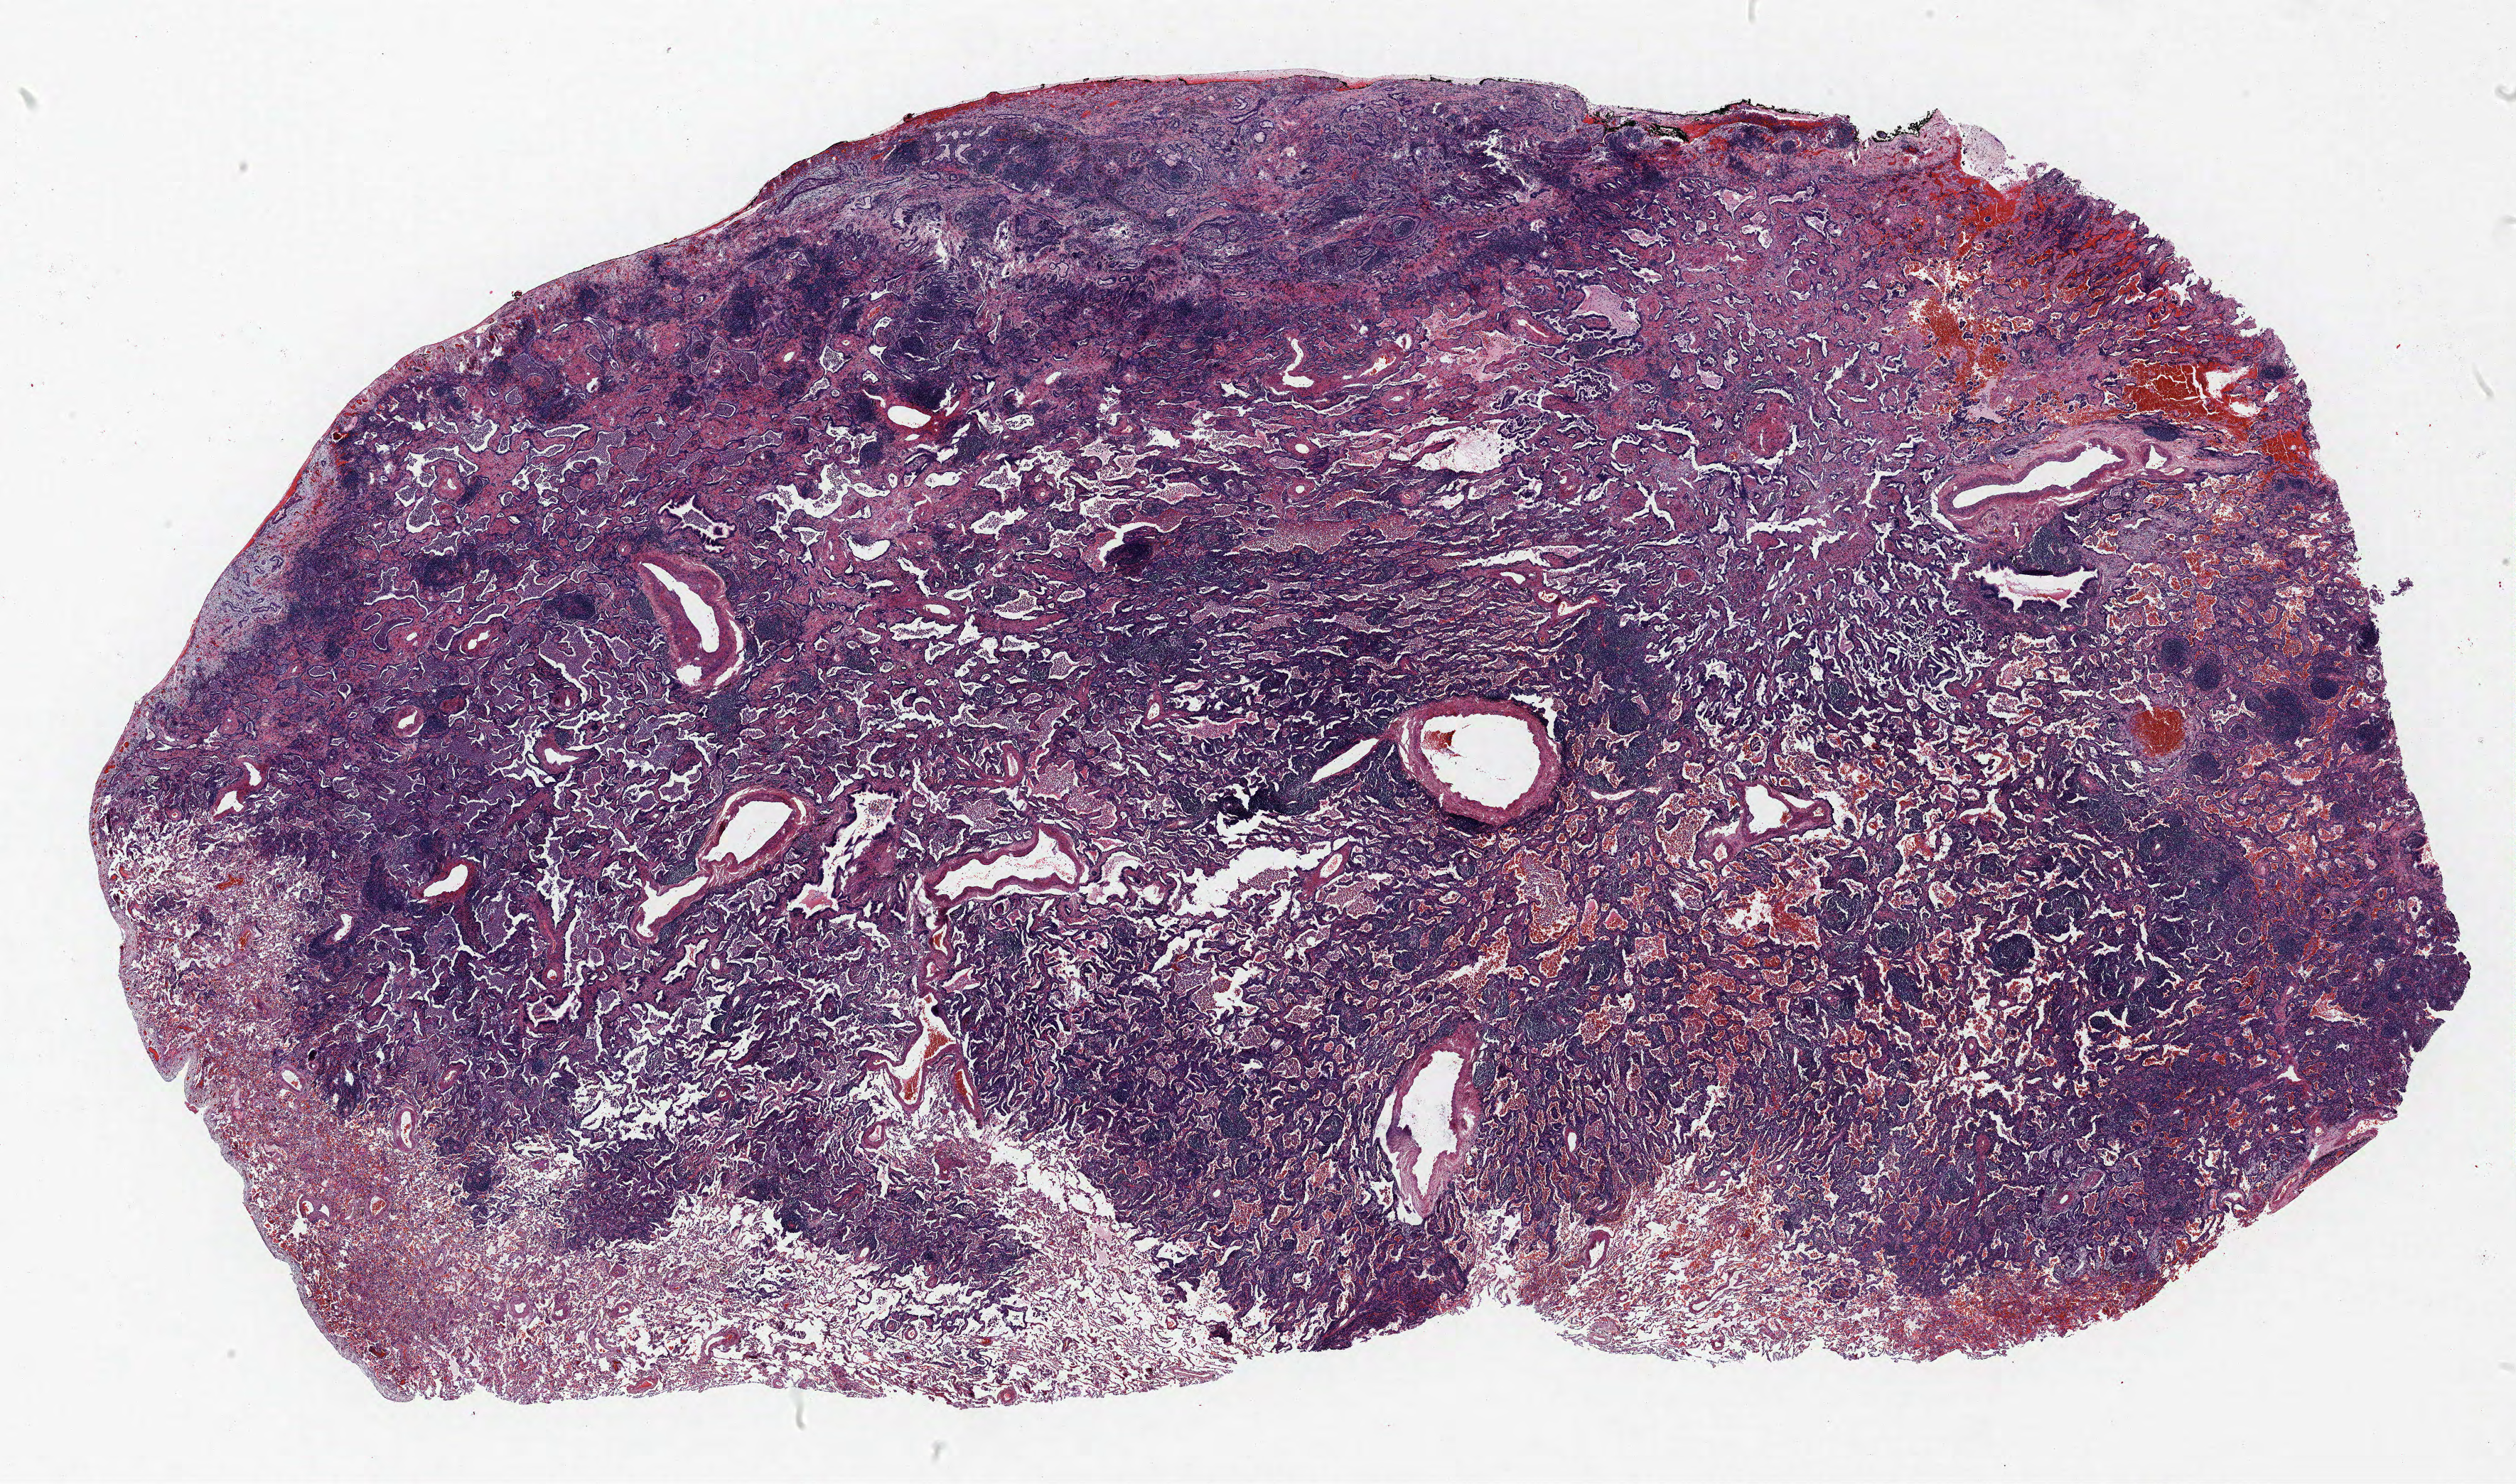
Whole-slide histology image, Hematoxylin and eosin (H&E) stained — a low-resolution overview of the entire scanned area, about 28.3 x 16.7 mm, formalin-fixed paraffin-embedded (FFPE) section, lung tissue. Male, age 61 at enrolment. Former smoker at enrolment.
* participant's lung-cancer diagnosis: Bronchiolo-alveolar adenocarcinoma, NOS
* tumour size (pathology): 21 mm
* primary tumour location (clinical record): right lower lobe
* ICD-O-3 topography: lower lobe of lung (C34.3)
* stage (AJCC 6th edition): IA